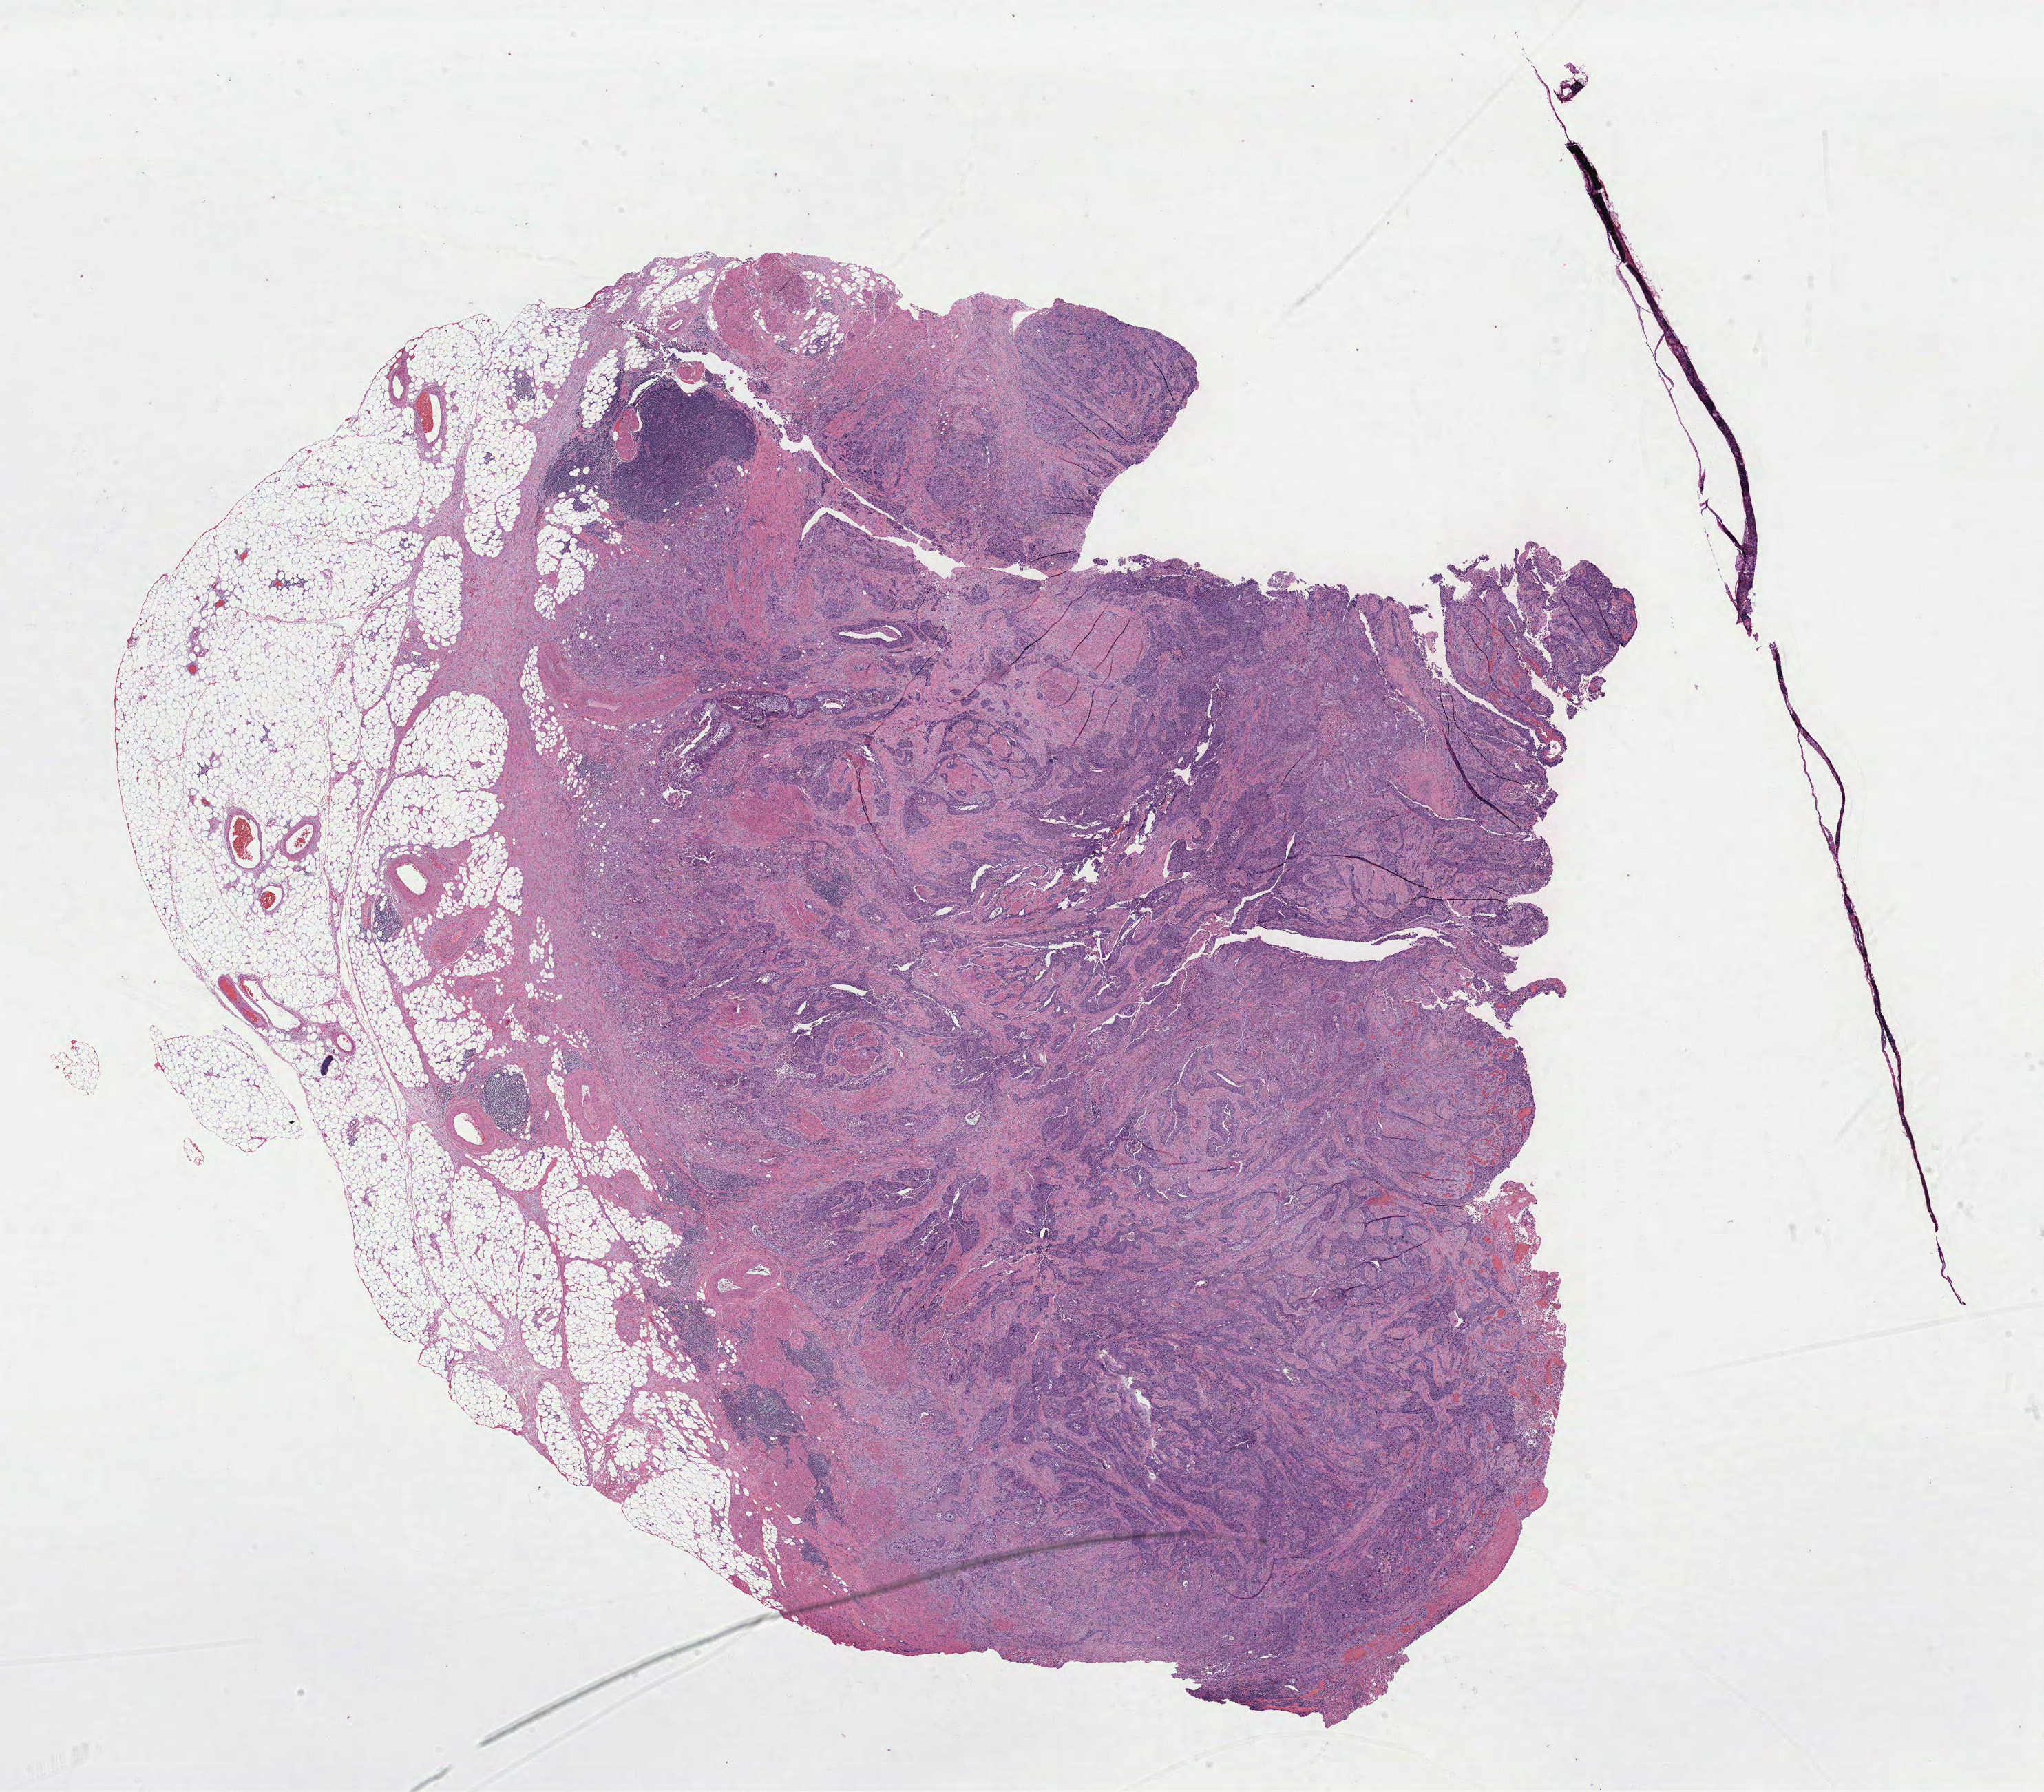
Digitized H&E-stained tissue section (whole slide), shown as a low-resolution overview of the whole scanned area (about 23.9 x 20.9 mm, acquisition: 40x scan). Formalin-fixed paraffin-embedded (FFPE) diagnostic section. Primary tumour sample from the bladder. Female, age 78 years at initial diagnosis.
Pathologic diagnosis: Transitional cell carcinoma.